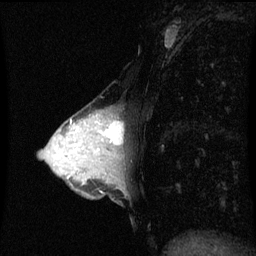
Breast MRI (dynamic contrast-enhanced), one sagittal slice. Position 29 of 60 along the scan axis. Dynamic contrast-enhanced series, image 2 of 3 at this slice position (ordered by acquisition). 1.5 T. TE 4.2 ms, TR 8.9 ms. 2 mm slice thickness. 256 × 256 image matrix, field of view 200 × 200 mm. Patient: female, 33 years. Case-level facts recorded for this patient, not image findings: setting: breast cancer imaged before/during neoadjuvant chemotherapy; receptor status: HER2-positive.
Outlined on this slice (semi-automatically segmented with operator editing):
- analysis volume of interest (the breast-tissue region the enhancement analysis was run in; not a lesion): bounding box (x1, y1, x2, y2) in pixels: (95, 112, 125, 153)
- tumour enhancement mask (voxels above the 70 % enhancement threshold inside the analysis volume of interest): (105, 122, 123, 145)